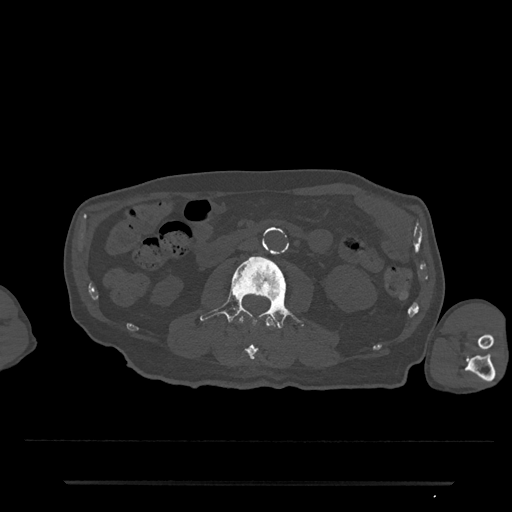
CT including the spine, one axial slice; slice 6 of 797 in the series (ordered by position); reconstruction kernel Br40s/3; 120 kVp; bone window (W 1800 / L 400 HU); 512 × 512 image matrix, field of view 427 × 427 mm. Patient: male, 74 years. From the clinical record (not read from this slice): primary cancer: prostate.
Structures marked on this image (semi-automatic segmentation, software-assisted and operator-edited):
- L2 vertebra: bounding box <237,314,278,361> (left, top, right, bottom; pixels)
- L3 vertebra: <200,256,304,329>